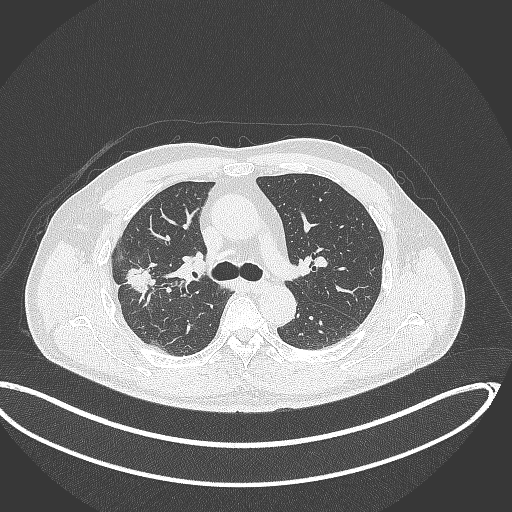
Chest CT, one axial slice. Position 223 of 391 along the scan axis. Reconstruction kernel B70f. Lung window (W 1500 / L -600 HU). 1 mm slice thickness. 512 × 512 image matrix, field of view 439 × 439 mm. Male patient, age 63 years. From the clinical record (not read from this slice): clinical TNM (as recorded): T1c N0 M0; histopathological grade: G2-3.
Outlined on this slice (bounding box drawn by a radiologist):
- lung tumour (recorded histology: adenocarcinoma): bounding box [x1, y1, x2, y2] px = [121, 257, 161, 305]